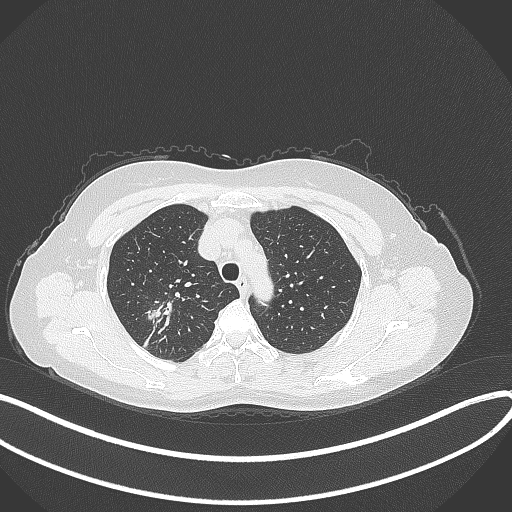
Chest CT, one axial slice; position 284 of 337 along the scan axis; 120 kVp; lung window (W 1500 / L -600 HU); 1 mm slice thickness; 512 × 512 image matrix, field of view 400 × 400 mm. Patient: female, 50 years. Case-level facts recorded for this patient, not image findings: clinical TNM (as recorded): T1c N0 M0.
Outlined on this slice (rectangle marked by the reading radiologist):
- lung tumour (recorded histology: adenocarcinoma): bounding box <138,300,172,322> (left, top, right, bottom; pixels)